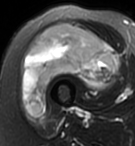
MRI of an extremity soft-tissue mass, one axial slice. Position 39 of 95 along the scan axis. T2-weighted fat-saturated. MR volume resampled by the dataset authors to the PET/CT grid (not the native acquisition matrix). 135 × 146 image matrix, field of view 132 × 143 mm. Female patient. From the clinical record (not read from this slice): histological type: pleiomorphic undifferentiated sarcoma; grade: high; site of the primary tumour: right quadricep.
Outlined on this slice (expert contour drawn on MRI and transferred to this co-registered scan by the dataset authors):
- gross tumour volume including surrounding oedema: bounding box (x1, y1, x2, y2) in pixels: (21, 25, 118, 117)
- gross tumour volume (mass): (21, 25, 118, 117)